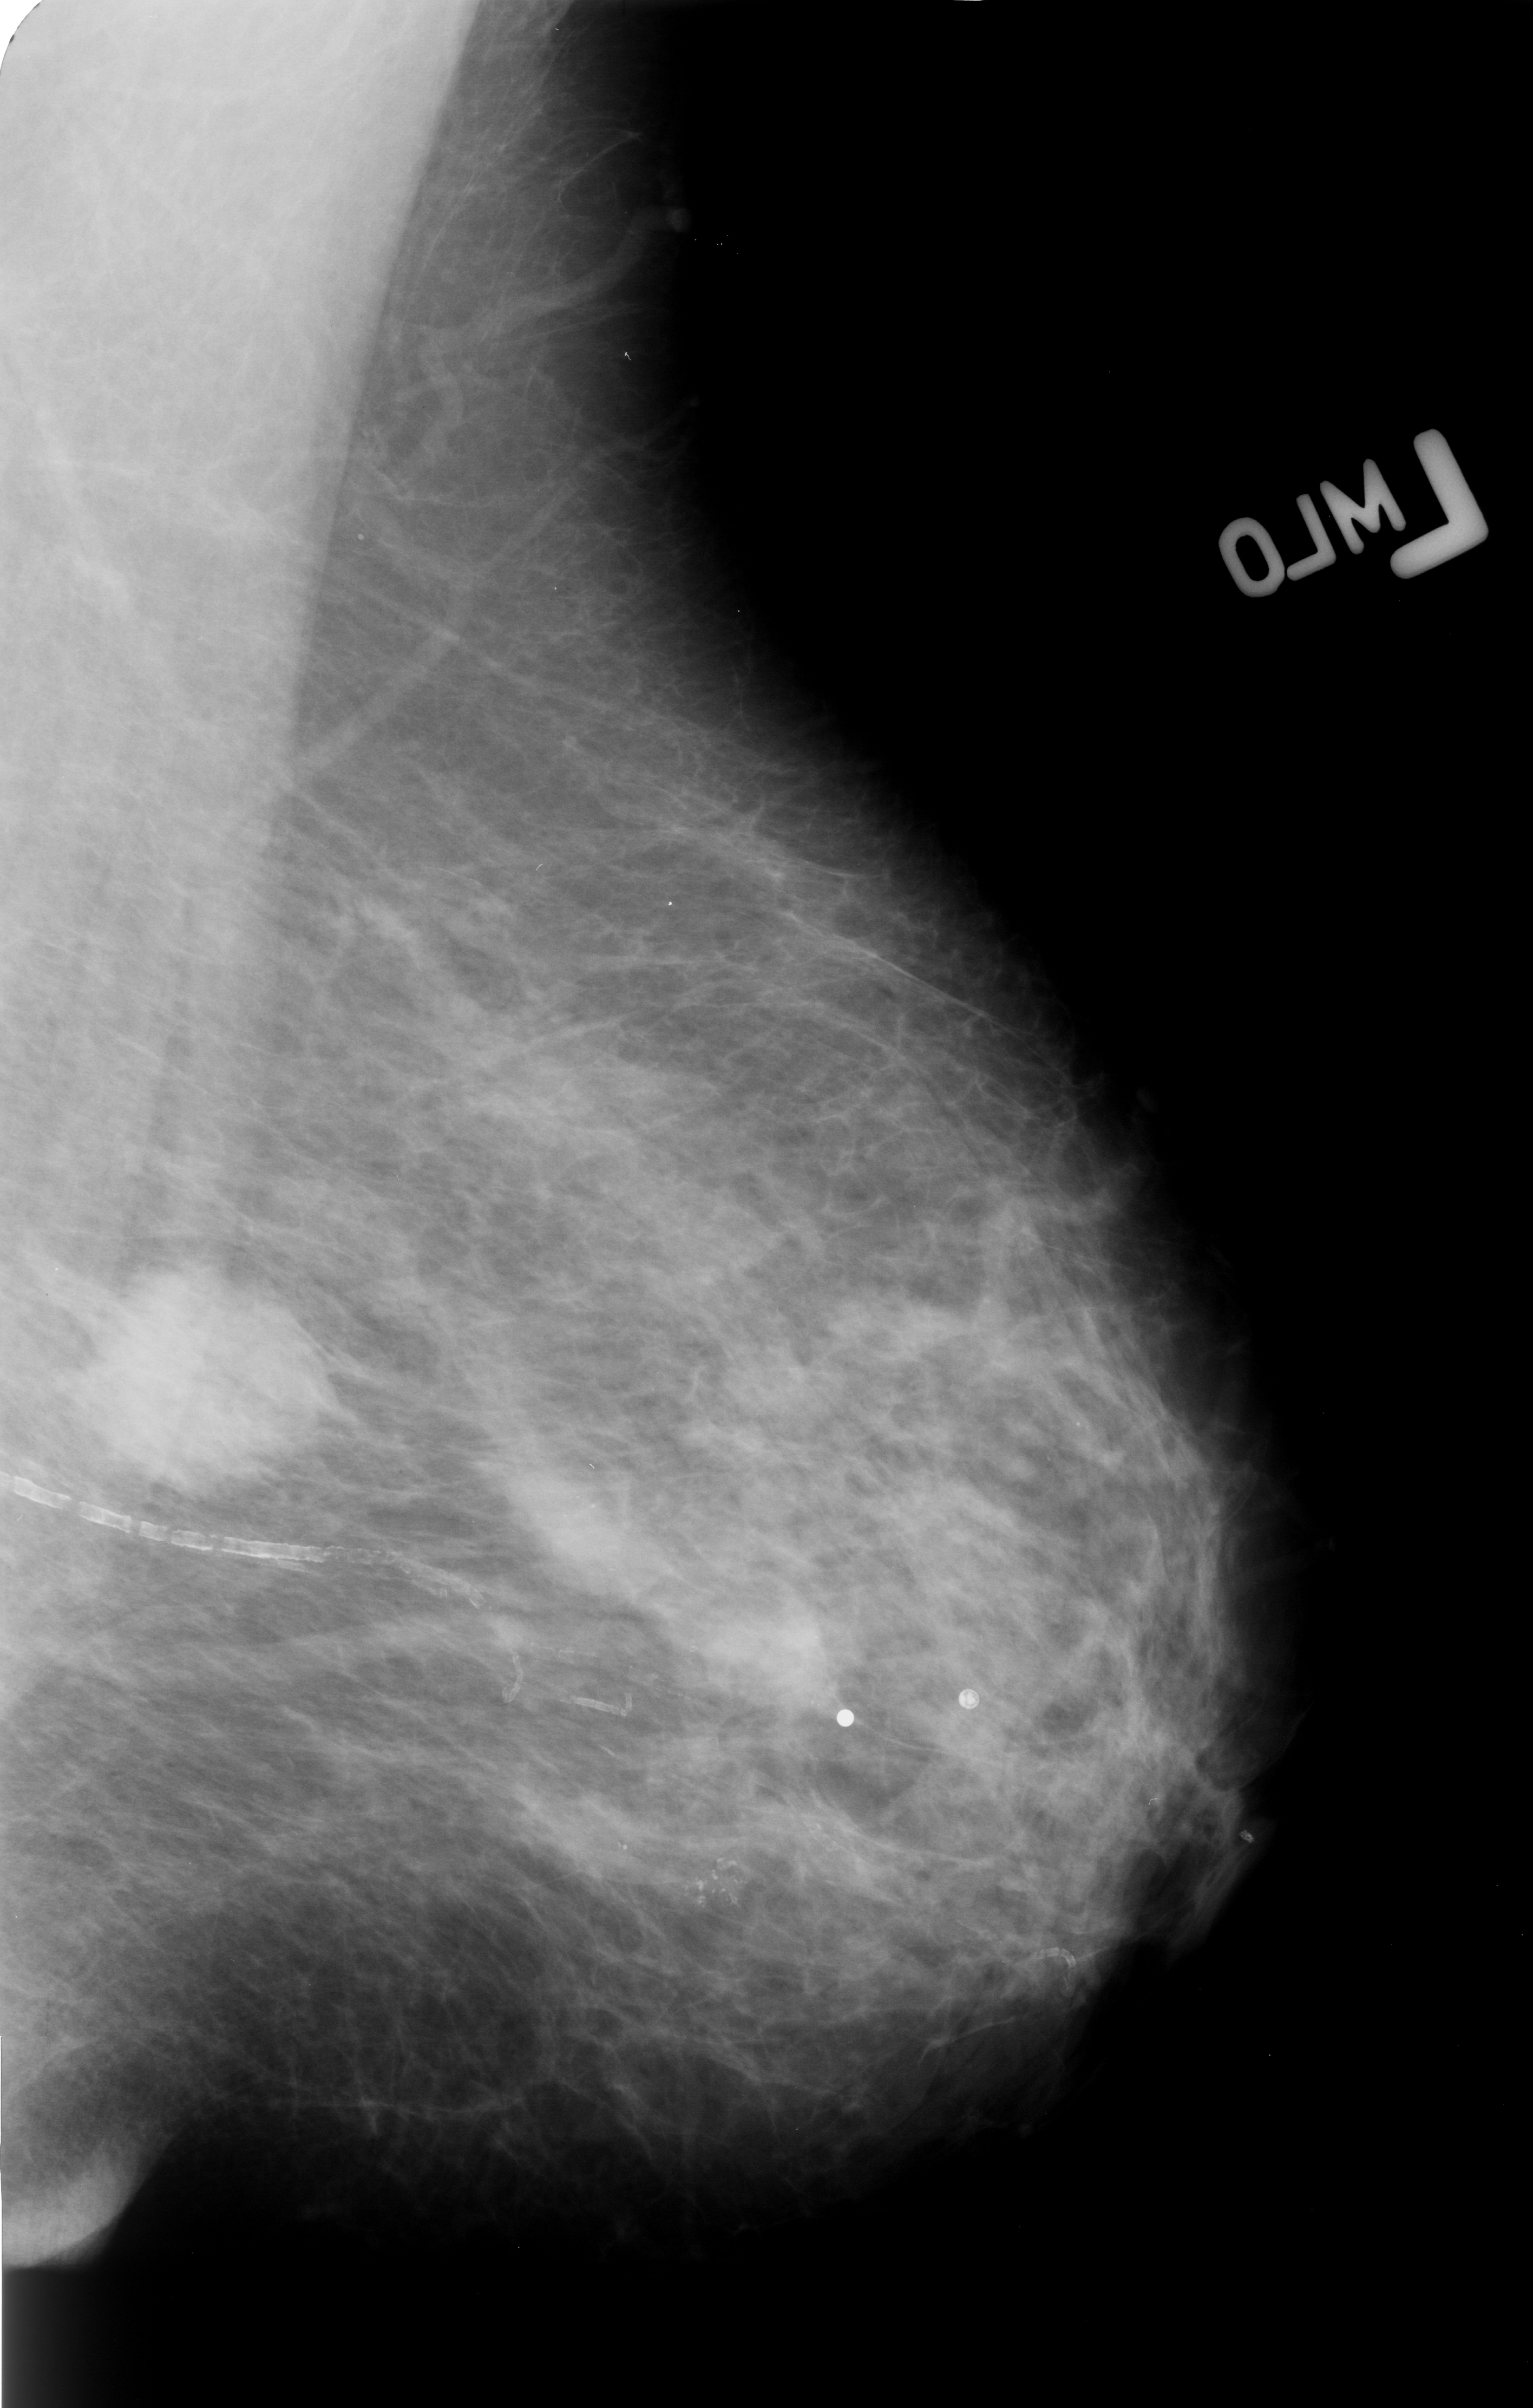
Scanned film-screen mammogram; left breast; MLO view; BI-RADS breast density category 2 (scale 1–4); 1533 × 2408 image matrix.
Marked abnormalities (boxes around the expert regions of interest):
- calcifications, distribution clustered; BI-RADS assessment category 4; subtlety rating 4 on a 1 (subtle) to 5 (obvious) scale; pathology result (as recorded, not read from the image): malignant: bounding box (x1, y1, x2, y2) in pixels: (17, 1221, 386, 1521)